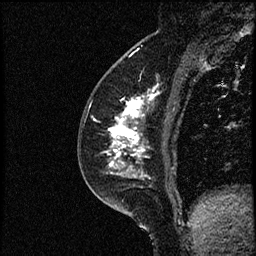
Breast MRI (dynamic contrast-enhanced), one sagittal slice; position 29 of 52 along the scan axis; dynamic contrast-enhanced study with each time point stored as its own series, time point 2 of 3 at this slice position (early post-contrast, ordered by acquisition time); 1.5 T; TE 4.2 ms, TR 17.6 ms; 256 × 256 image matrix, field of view 200 × 200 mm. Female patient, age 49 years. From the clinical record (not read from this slice): setting: breast cancer imaged before/during neoadjuvant chemotherapy; receptor status: HER2-positive.
Structures marked on this image (semi-automatically segmented with operator editing):
- analysis volume of interest (the breast-tissue region the enhancement analysis was run in; not a lesion): bounding box (x1, y1, x2, y2) in pixels: (85, 65, 182, 175)
- tumour enhancement mask (voxels above the 100 % enhancement threshold inside the analysis volume of interest): (107, 90, 157, 175)